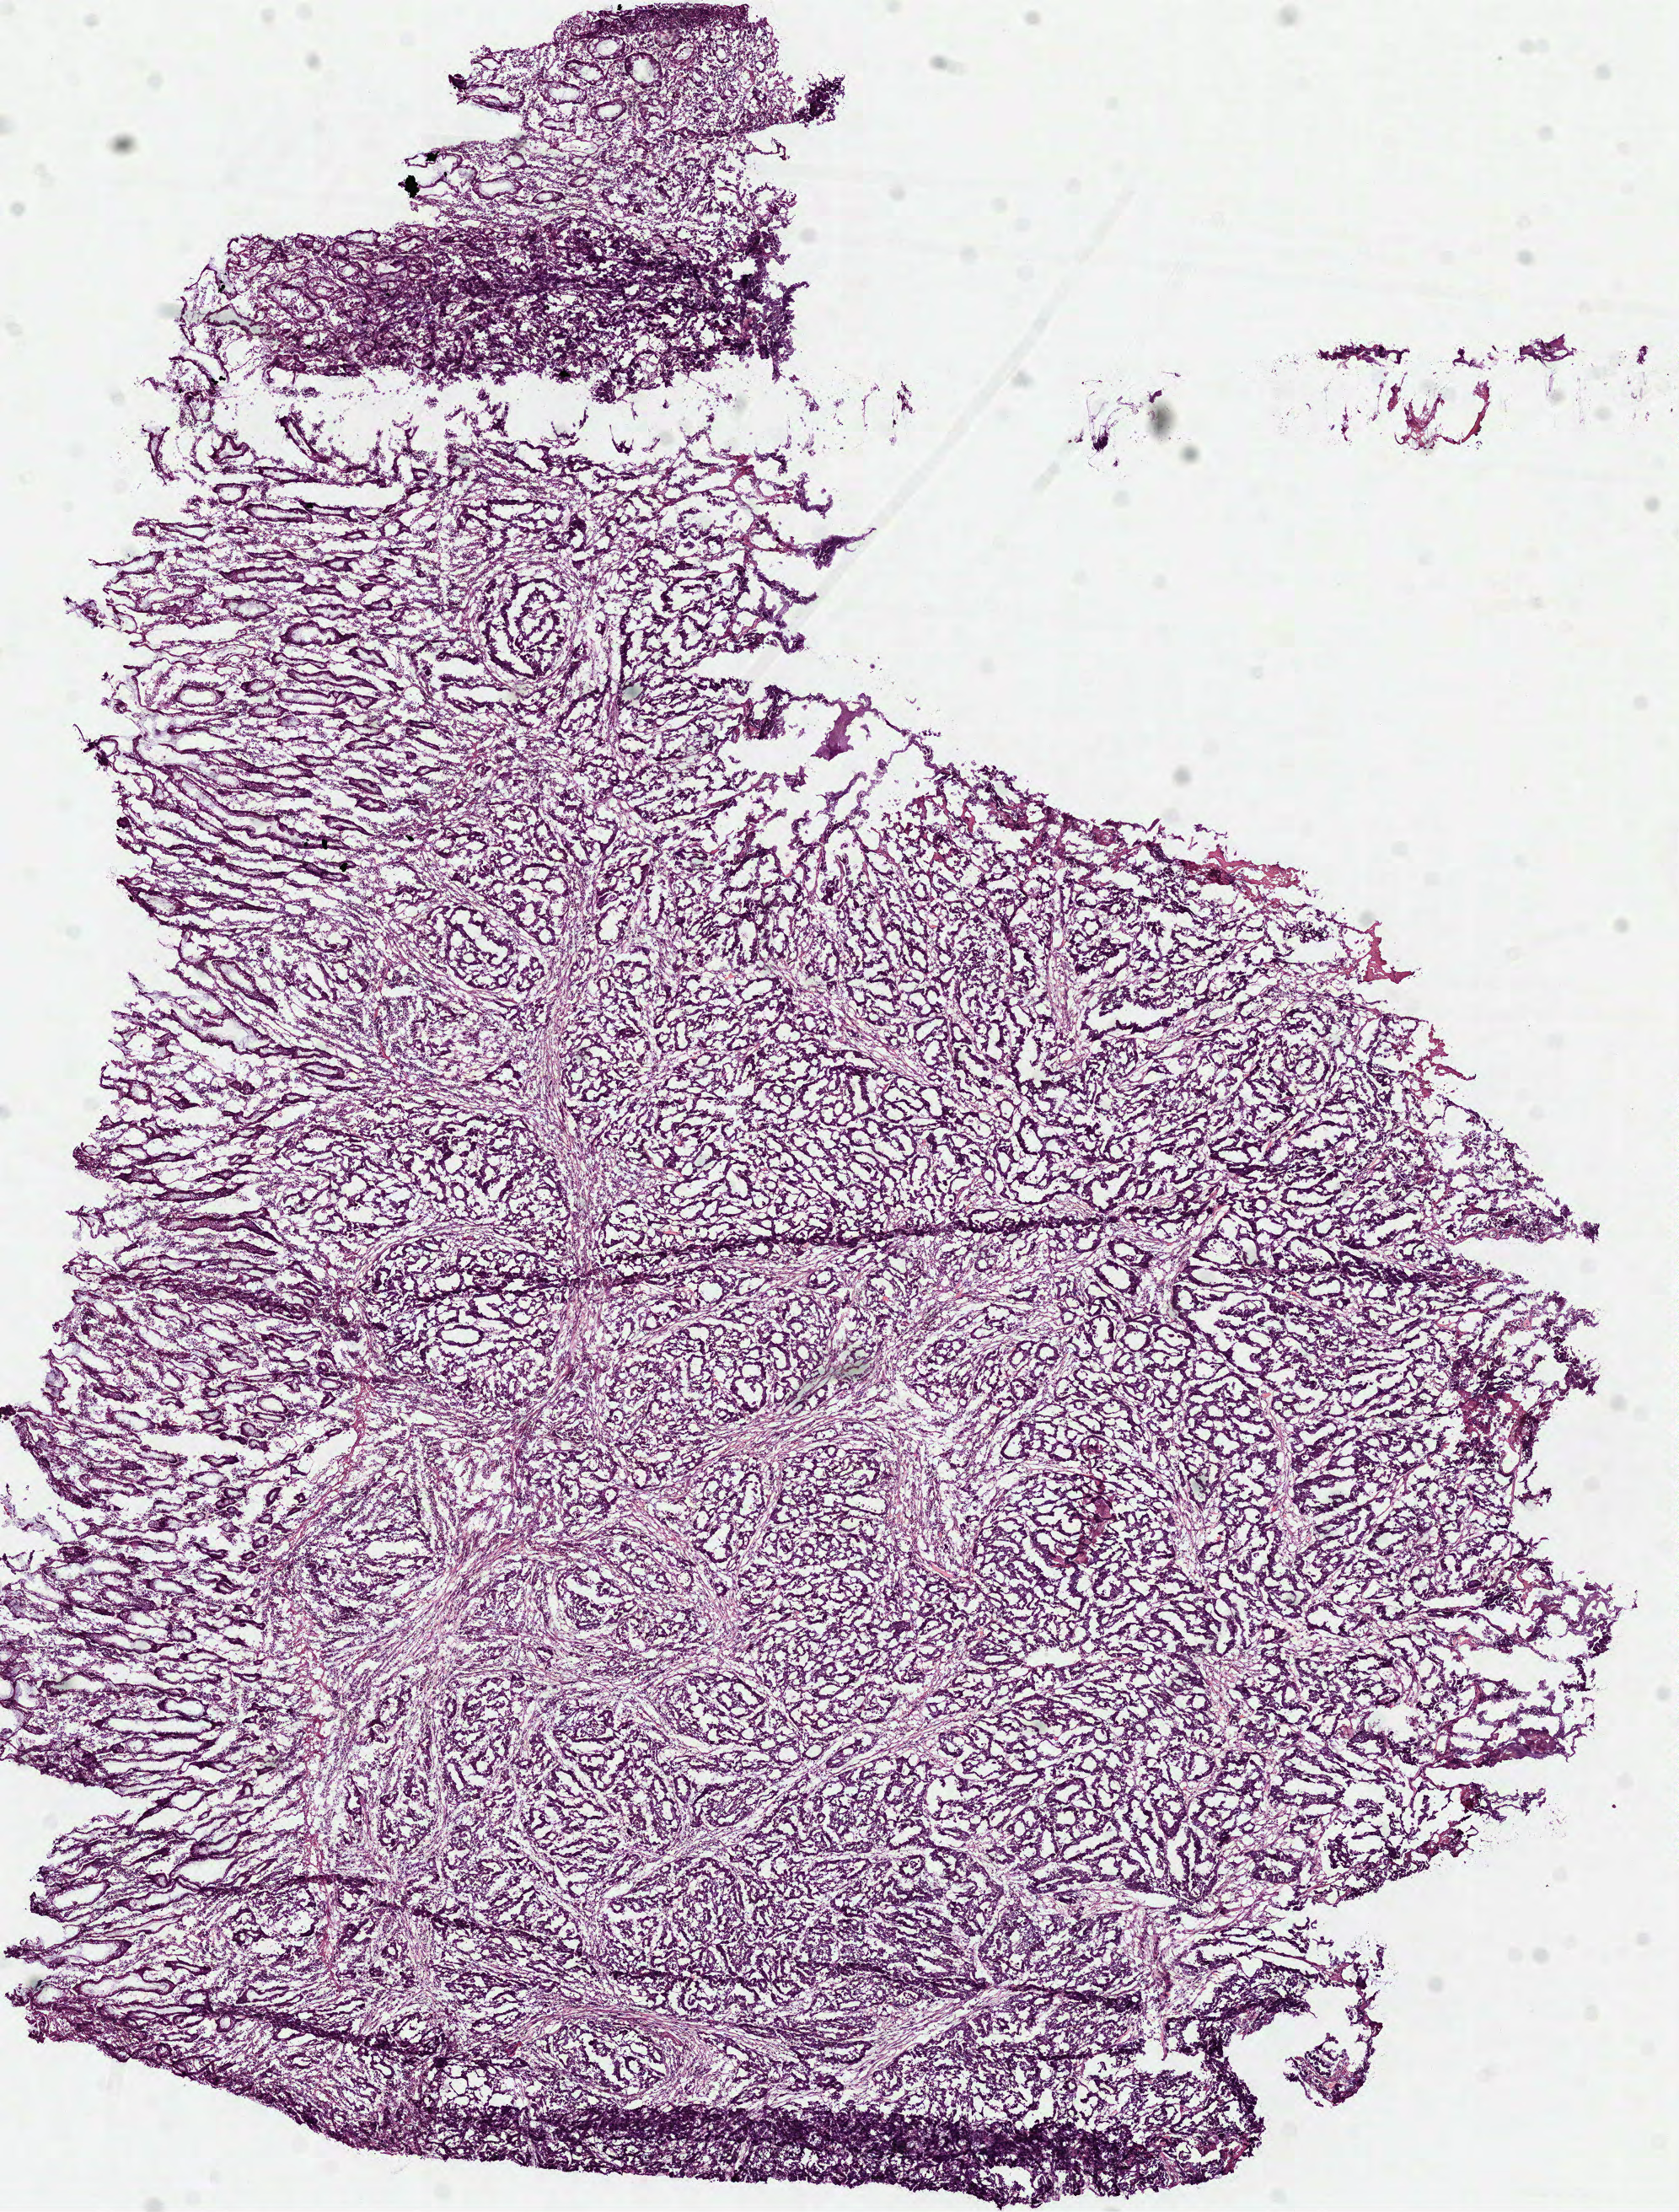
H&E-stained whole-slide image, shown as a low-resolution overview of the whole scanned area (about 8.0 x 10.6 mm); frozen section from the top of the tissue portion; colon, primary tumour sample. Male patient.
Histologic diagnosis: Adenocarcinoma, NOS (ascending colon).